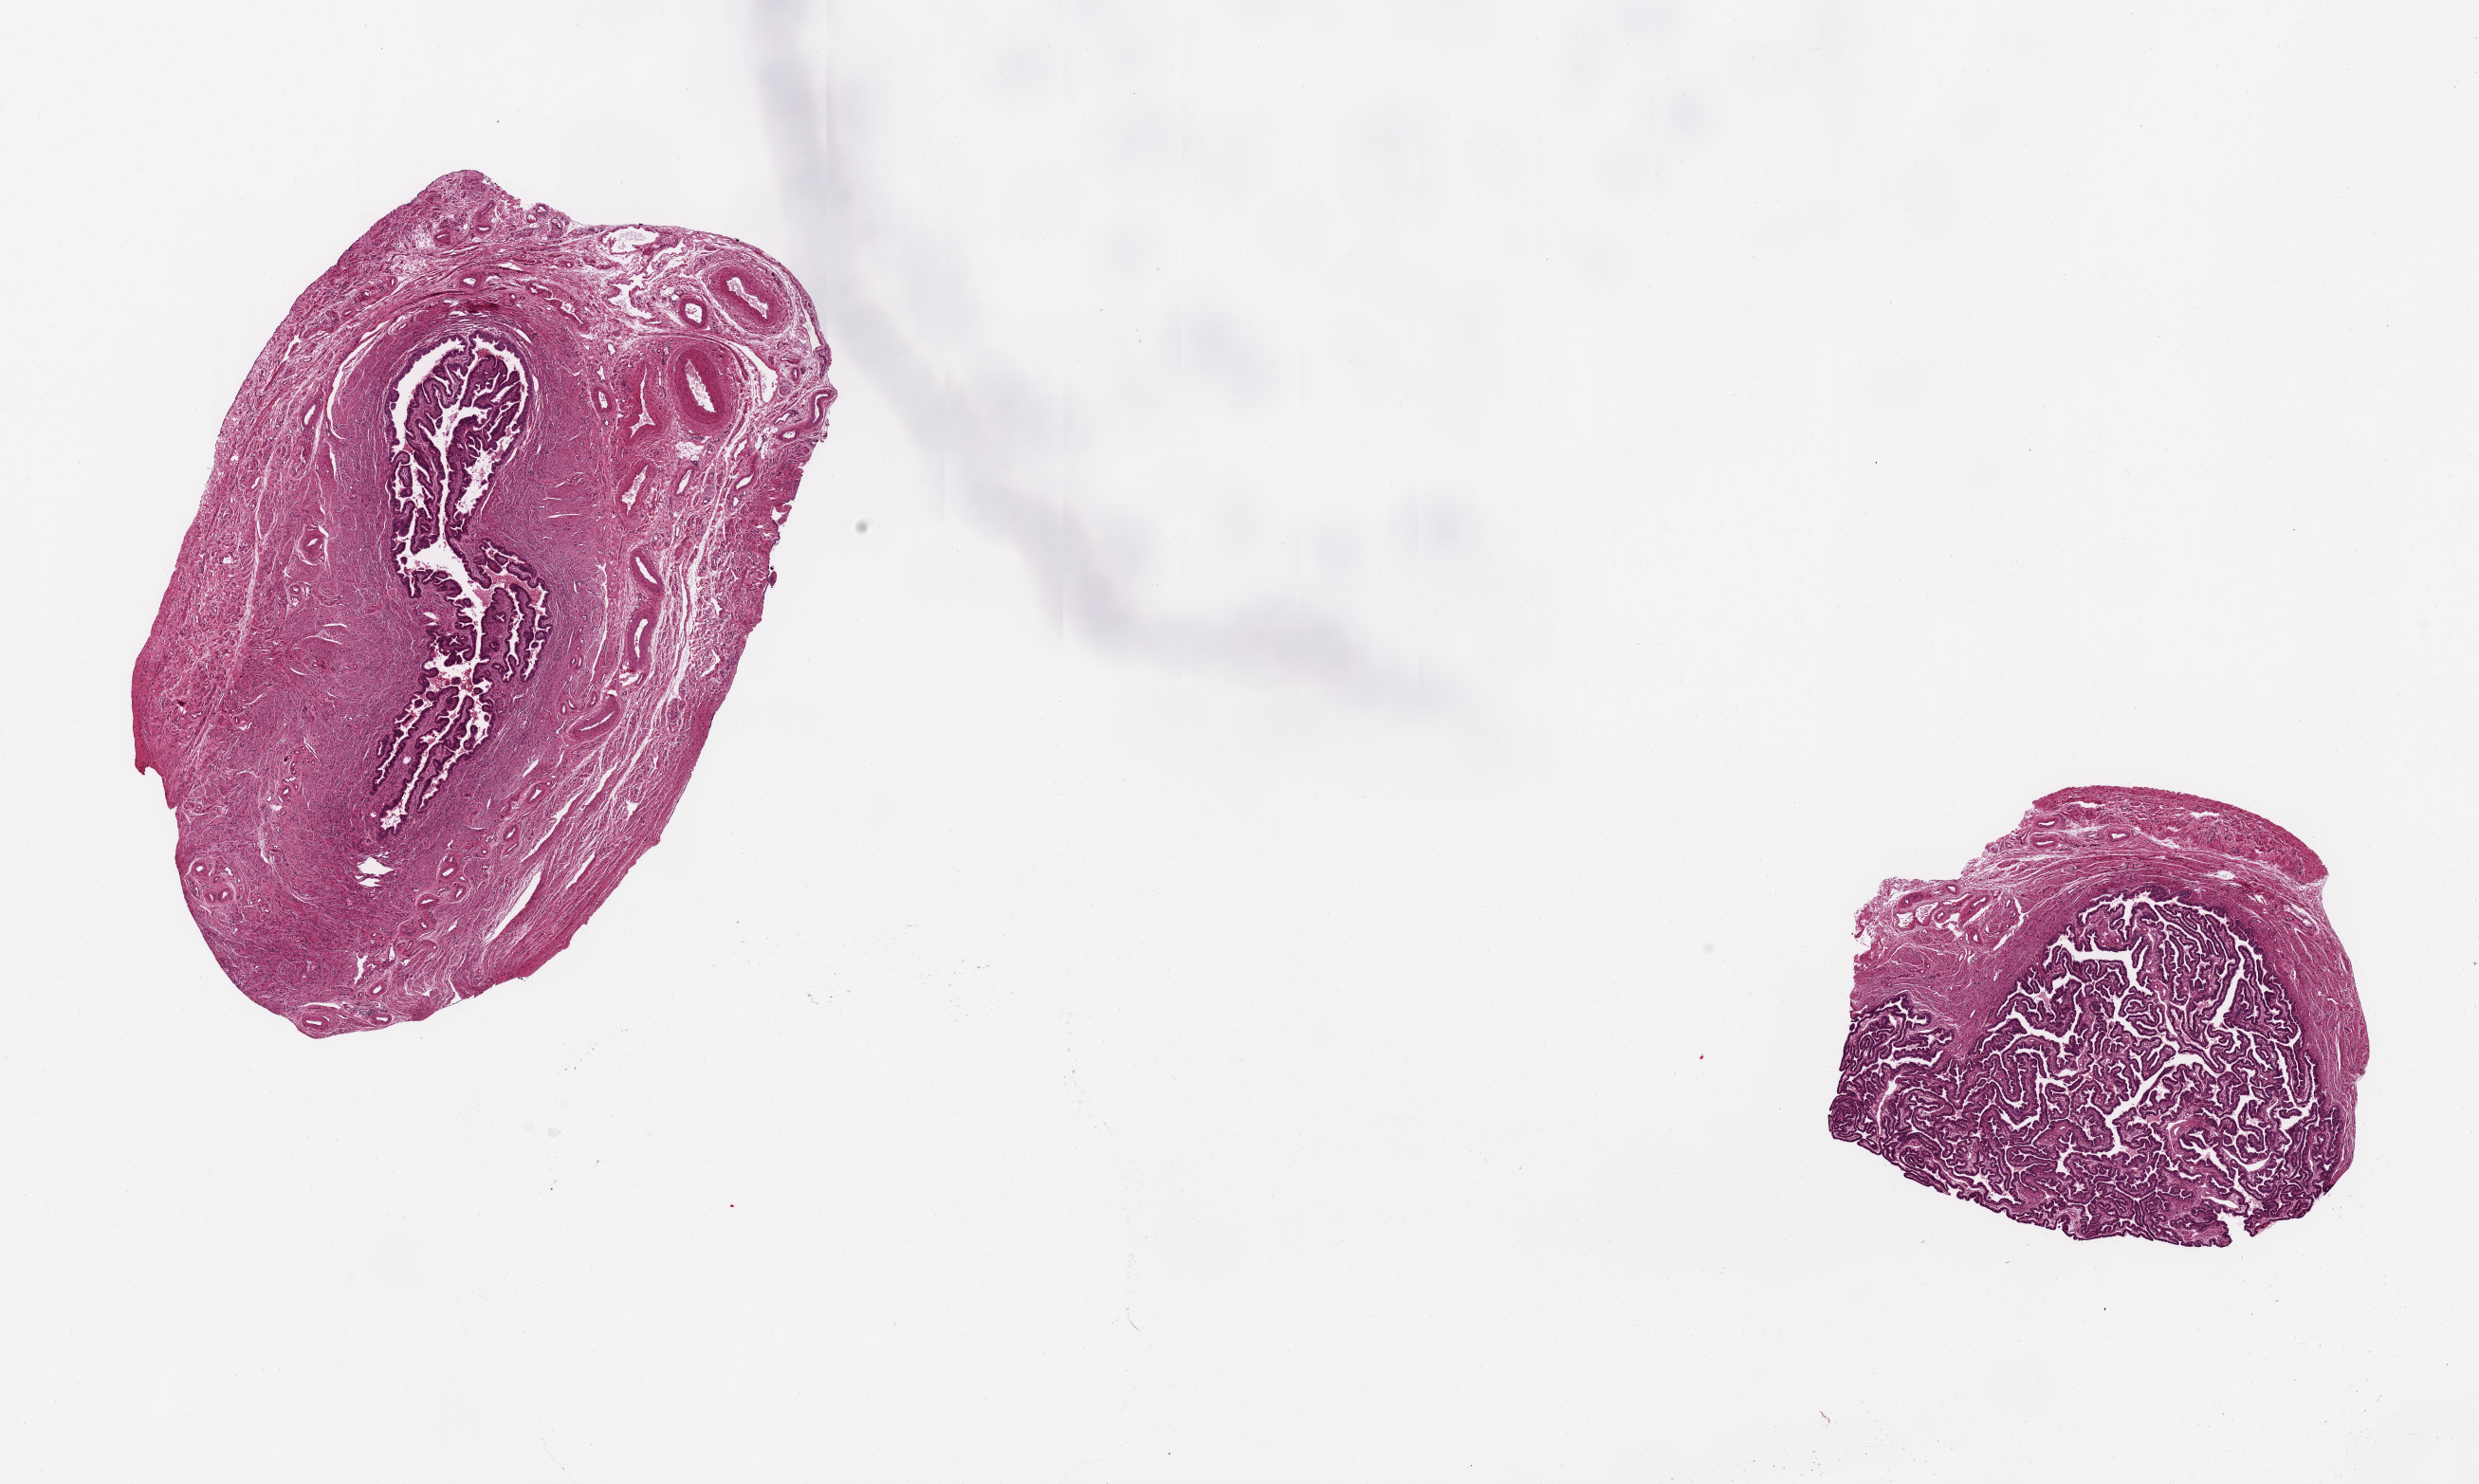
Whole-slide image, H&E stain, whole scanned area (about 20.7 x 12.4 mm) shown as a low-resolution overview; PAXgene-fixed paraffin-embedded (PFPE) section; target tissue: fallopian tube; tissue donor sample. Donor: female.
Reviewer comment on this tissue sample: 2 pieces, ~7x4 & 4x4mm with abundant well preserved epithelium.